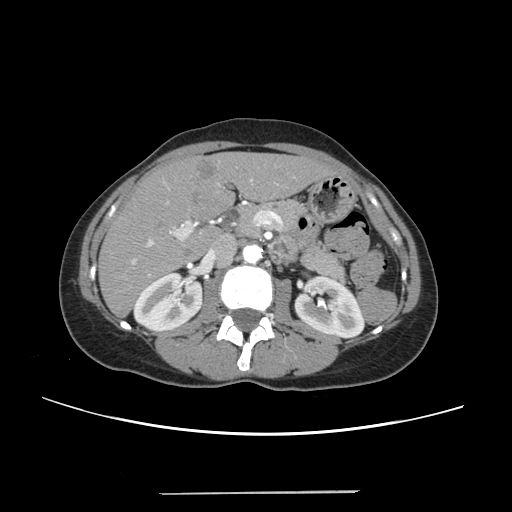
Contrast-enhanced abdominal CT, one axial slice; slice 122 of 240 in the series (ordered by position); intravenous contrast given; soft-tissue window (W 400 / L 40 HU); 1.25 mm slice thickness; 512 × 512 image matrix, field of view 371 × 371 mm. Female patient, age 60 years. Case-level facts recorded for this patient, not image findings: diagnosis: colorectal cancer liver metastases, imaged before liver resection; multiple liver metastases: no; largest metastasis: 1.5 cm; chemotherapy before resection: yes.
Annotated regions visible in this slice (expert manual segmentation):
- liver: box from (x=100, y=153) to (x=329, y=314) px
- planned liver remnant (the part of the liver to remain after resection): (x=100, y=154)–(x=330, y=314)
- portal vein (with intrahepatic branches): (x=131, y=179)–(x=278, y=276)
- liver metastasis: (x=196, y=160)–(x=218, y=181)